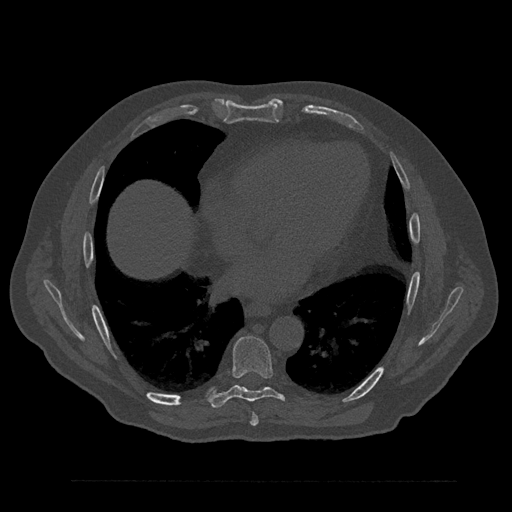
CT including the spine, one axial slice; position 455 of 797 along the scan axis; reconstruction kernel Br40s/3; bone window (W 1800 / L 400 HU); 512 × 512 image matrix, field of view 430 × 430 mm. Male patient, age 61 years. Case-level facts recorded for this patient, not image findings: primary cancer: prostate.
Outlined on this slice (semi-automatically segmented with operator editing):
- T7 vertebra: bounding box [x1, y1, x2, y2] px = [250, 413, 259, 426]
- T8 vertebra: [209, 336, 285, 408]